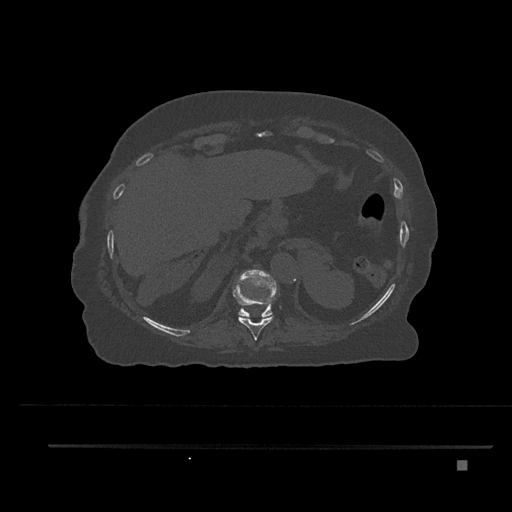
CT including the spine, one axial slice; slice 339 of 797 in the series (ordered by position); 120 kVp; bone window (W 1800 / L 400 HU); 0.5 mm slice thickness; 512 × 512 image matrix, field of view 437 × 437 mm. Patient: female, 76 years. Case-level facts recorded for this patient, not image findings: primary cancer: lung; vertebrae with lytic lesions (as recorded): T11, L3.
Annotated regions visible in this slice (semi-automatic segmentation, software-assisted and operator-edited):
- T10 vertebra: bounding box <233,284,275,340> (left, top, right, bottom; pixels)
- T11 vertebra: <238,269,277,317>